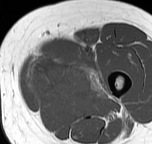
MRI of an extremity soft-tissue mass, one axial slice. Position 18 of 57 along the scan axis. MR volume resampled by the dataset authors to the PET/CT grid (not the native acquisition matrix). 3.27 mm slice thickness. 152 × 144 image matrix. Female patient. Case-level facts recorded for this patient, not image findings: histological type: pleiomorphic leiomyosarcoma; grade: intermediate; site of the primary tumour: left thigh.
Outlined on this slice (expert contour drawn on MRI and transferred to this co-registered scan by the dataset authors):
- gross tumour volume including surrounding oedema: bounding box [x1, y1, x2, y2] px = [25, 51, 106, 102]
- gross tumour volume (mass): [27, 53, 94, 102]